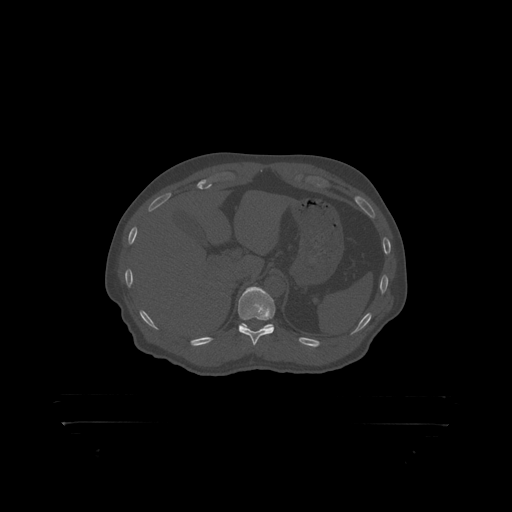
CT including the spine, one axial slice; position 373 of 399 along the scan axis; reconstruction kernel STANDARD; 120 kVp; bone window (W 1800 / L 400 HU); 1.25 mm slice thickness; 512 × 512 image matrix, field of view 650 × 650 mm. Patient: male, 46 years. From the clinical record (not read from this slice): primary cancer: skin.
Outlined on this slice (semi-automatically segmented with operator editing):
- T11 vertebra: bounding box <238,287,276,319> (left, top, right, bottom; pixels)